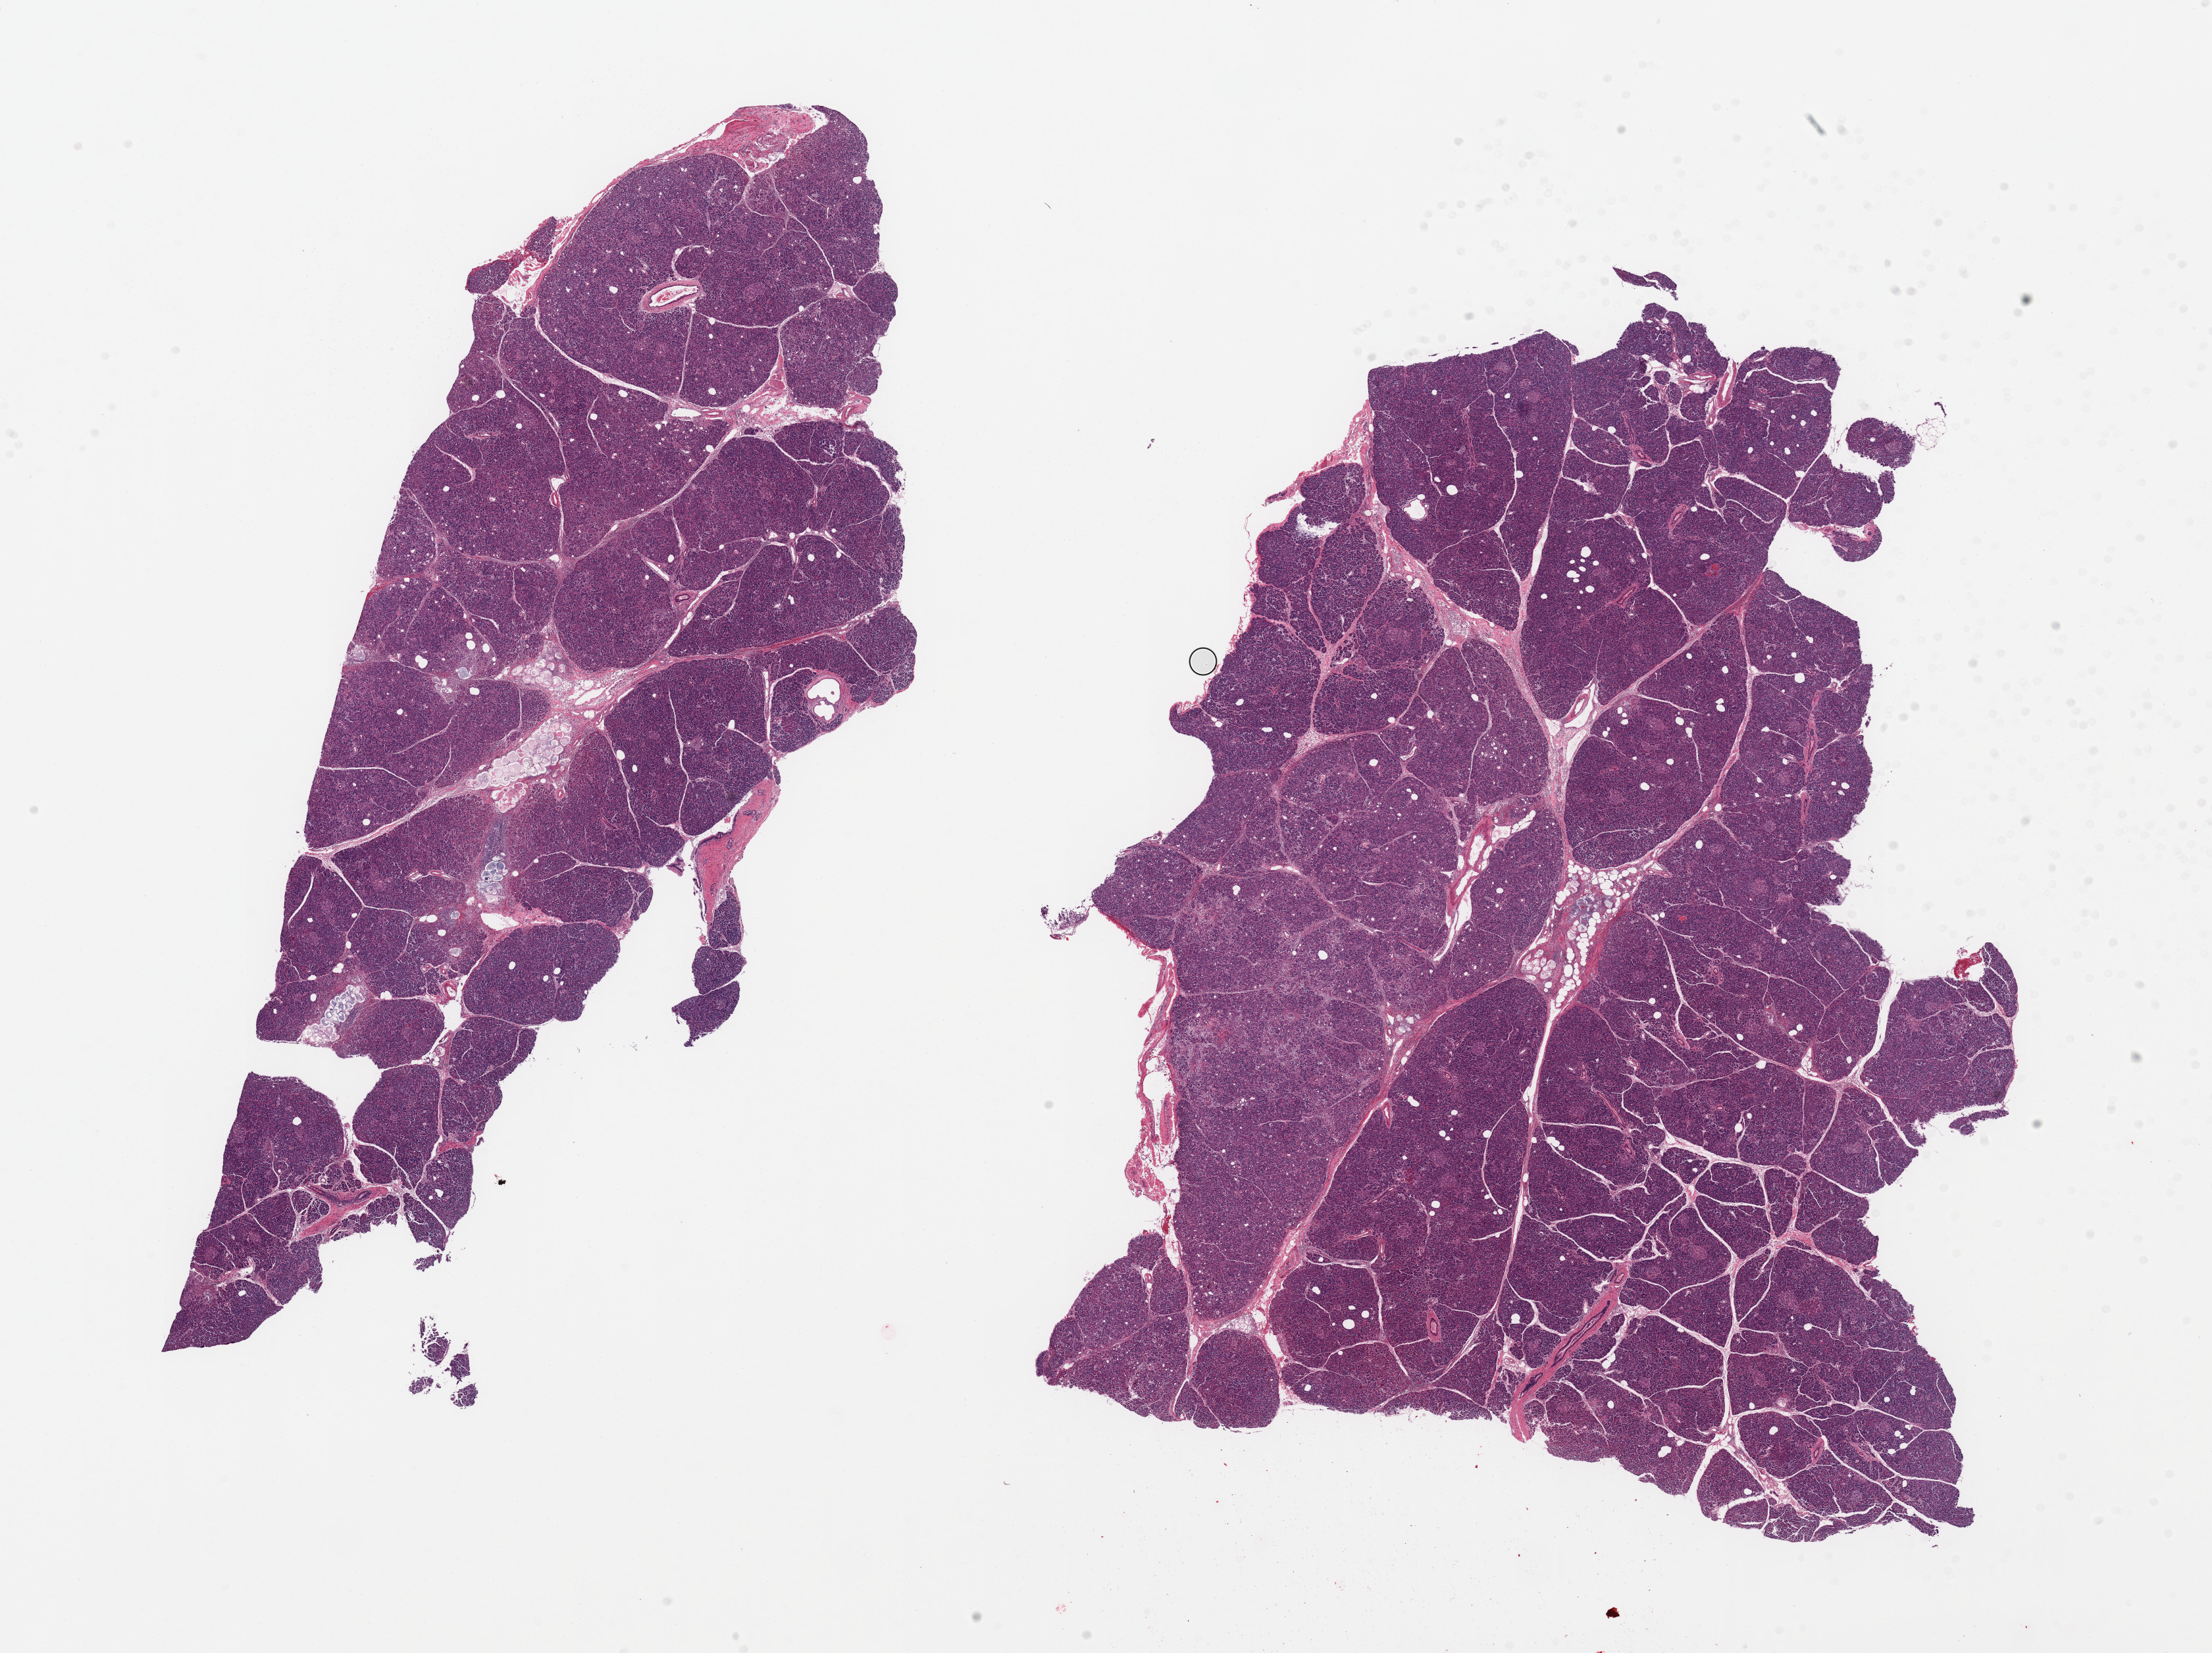
Whole-slide image, H&E stain, whole scanned area (about 26.6 x 19.9 mm) shown as a low-resolution overview, PAXgene-fixed paraffin-embedded (PFPE) section, sampled site (target tissue): pancreas, donor tissue sample. Male donor.
Reviewer comment on this tissue sample: 2 pieces; acute pancreatitis.